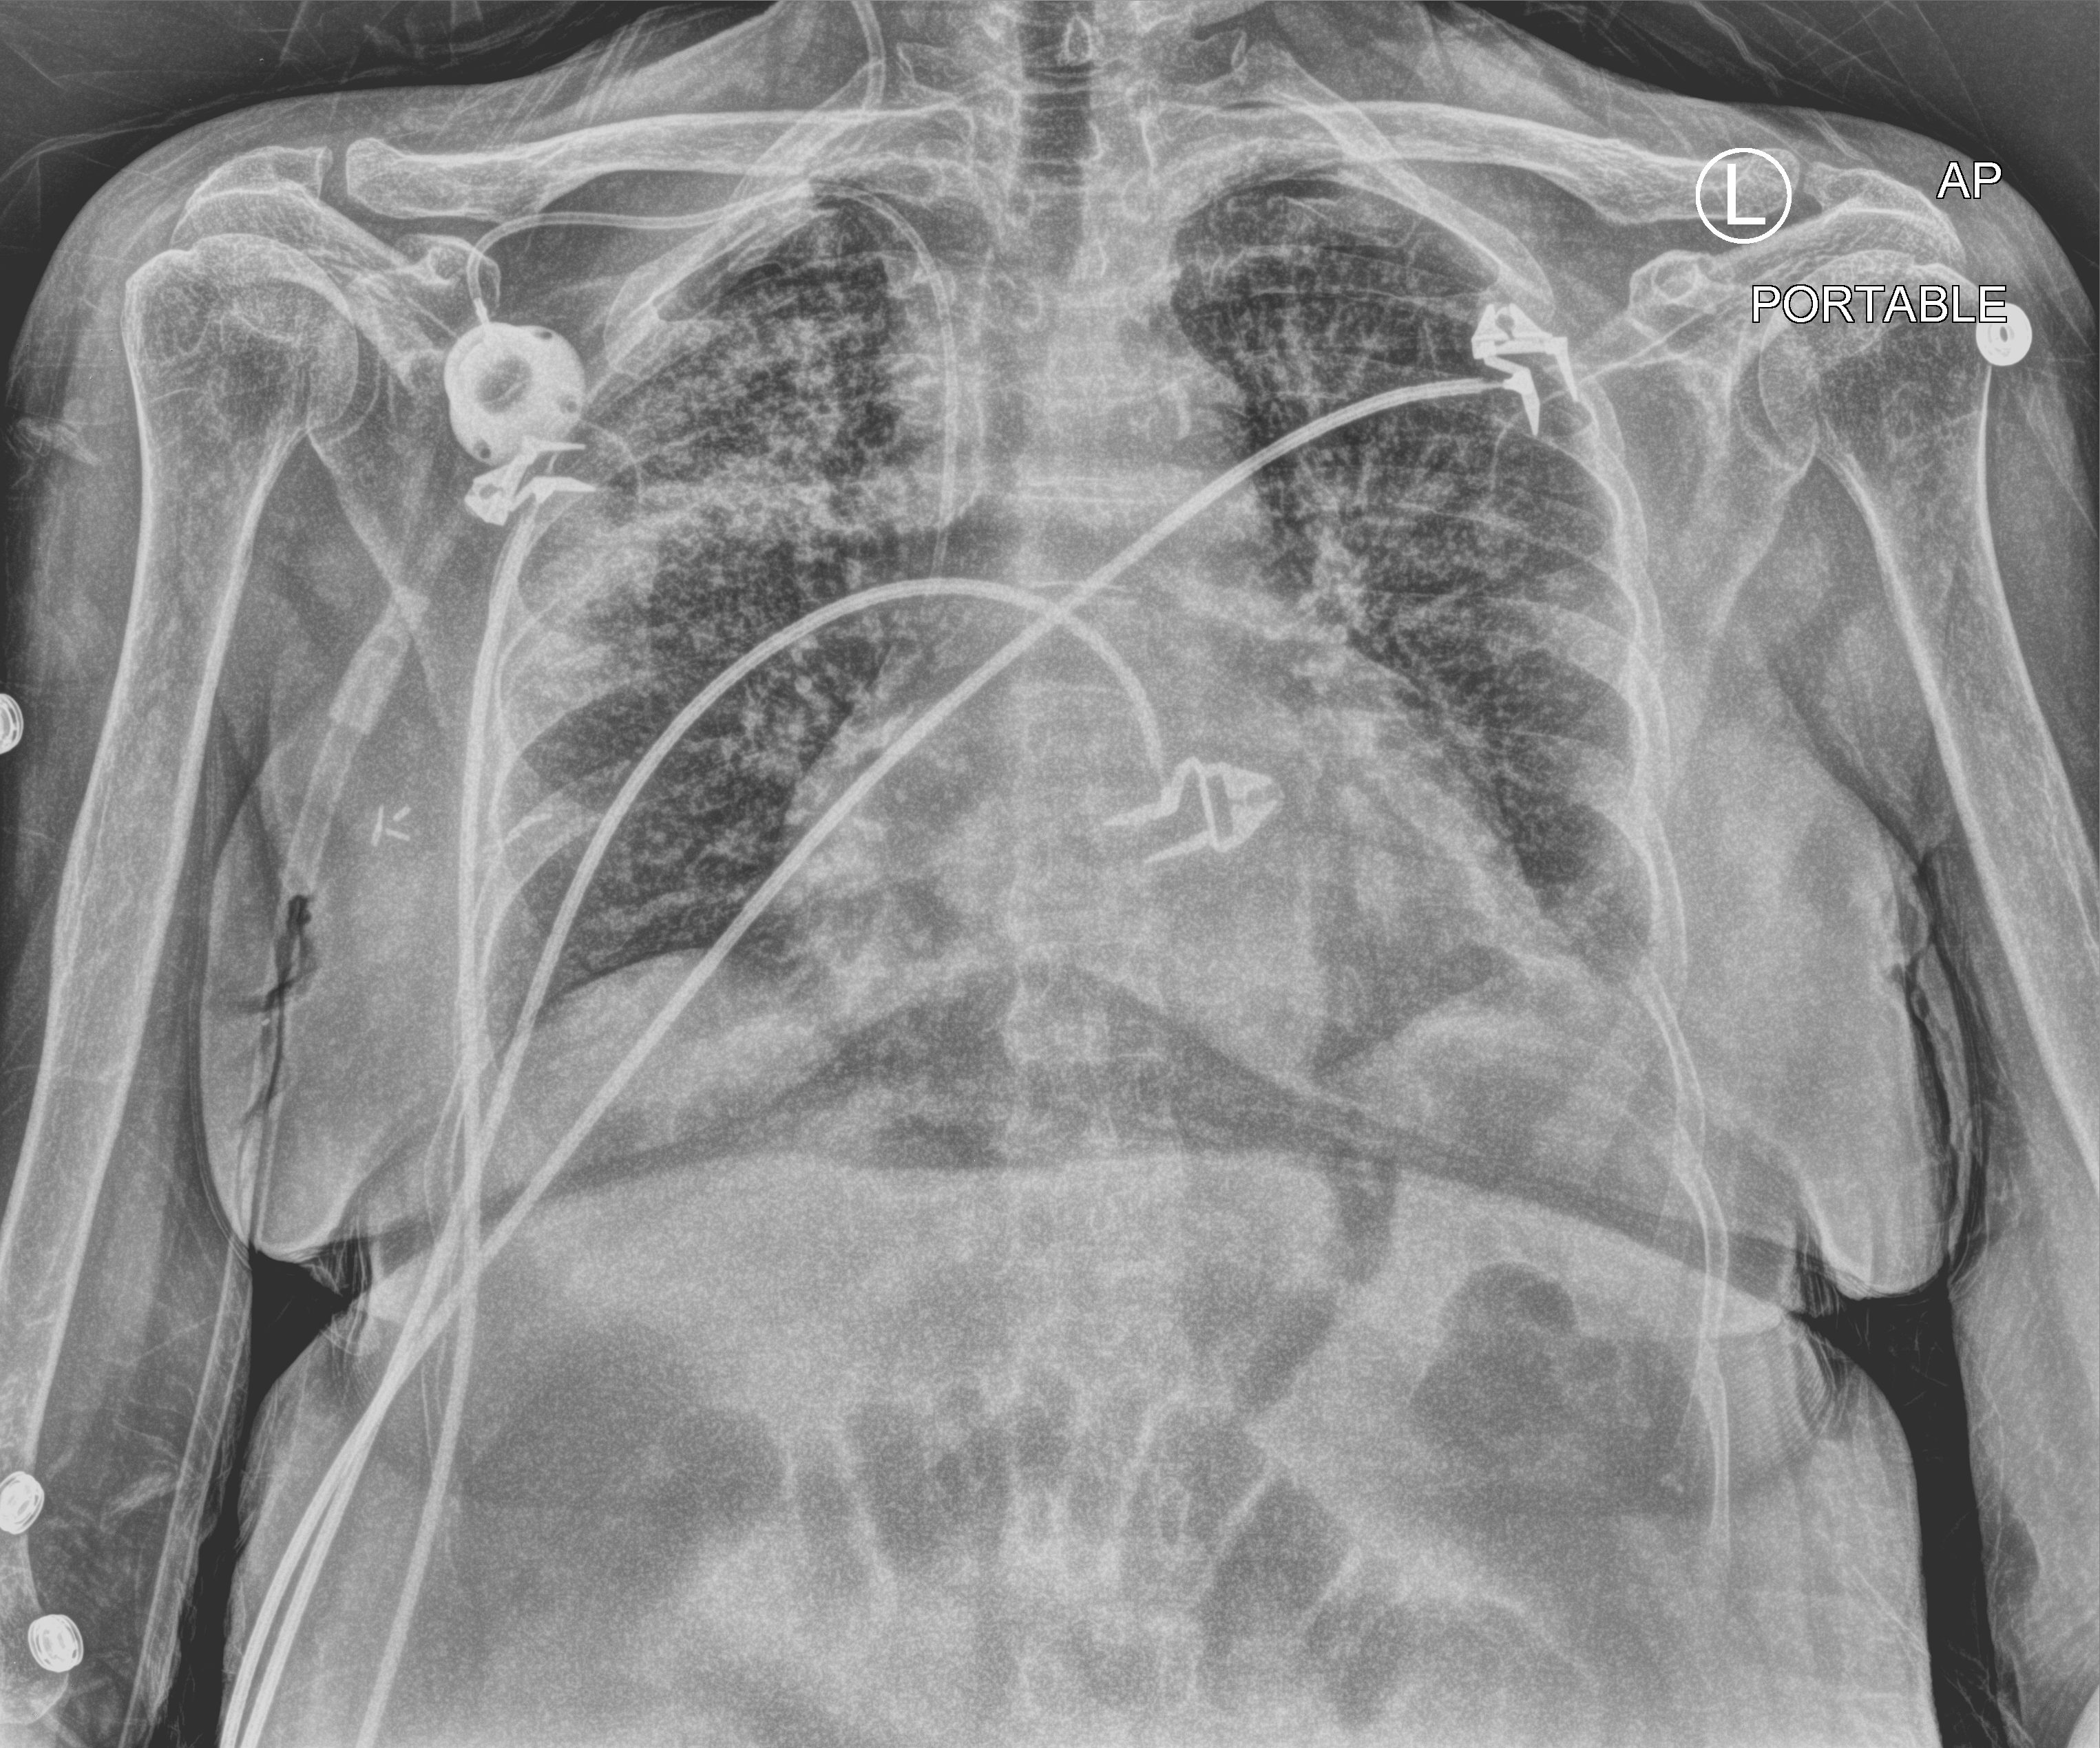
Portable chest radiograph. Female patient hospitalised with COVID-19, age 60–74 years.
From the hospital-stay record, not from the radiograph (when in the stay this image was taken is not recorded): other chronic lung disease (admission record): no.